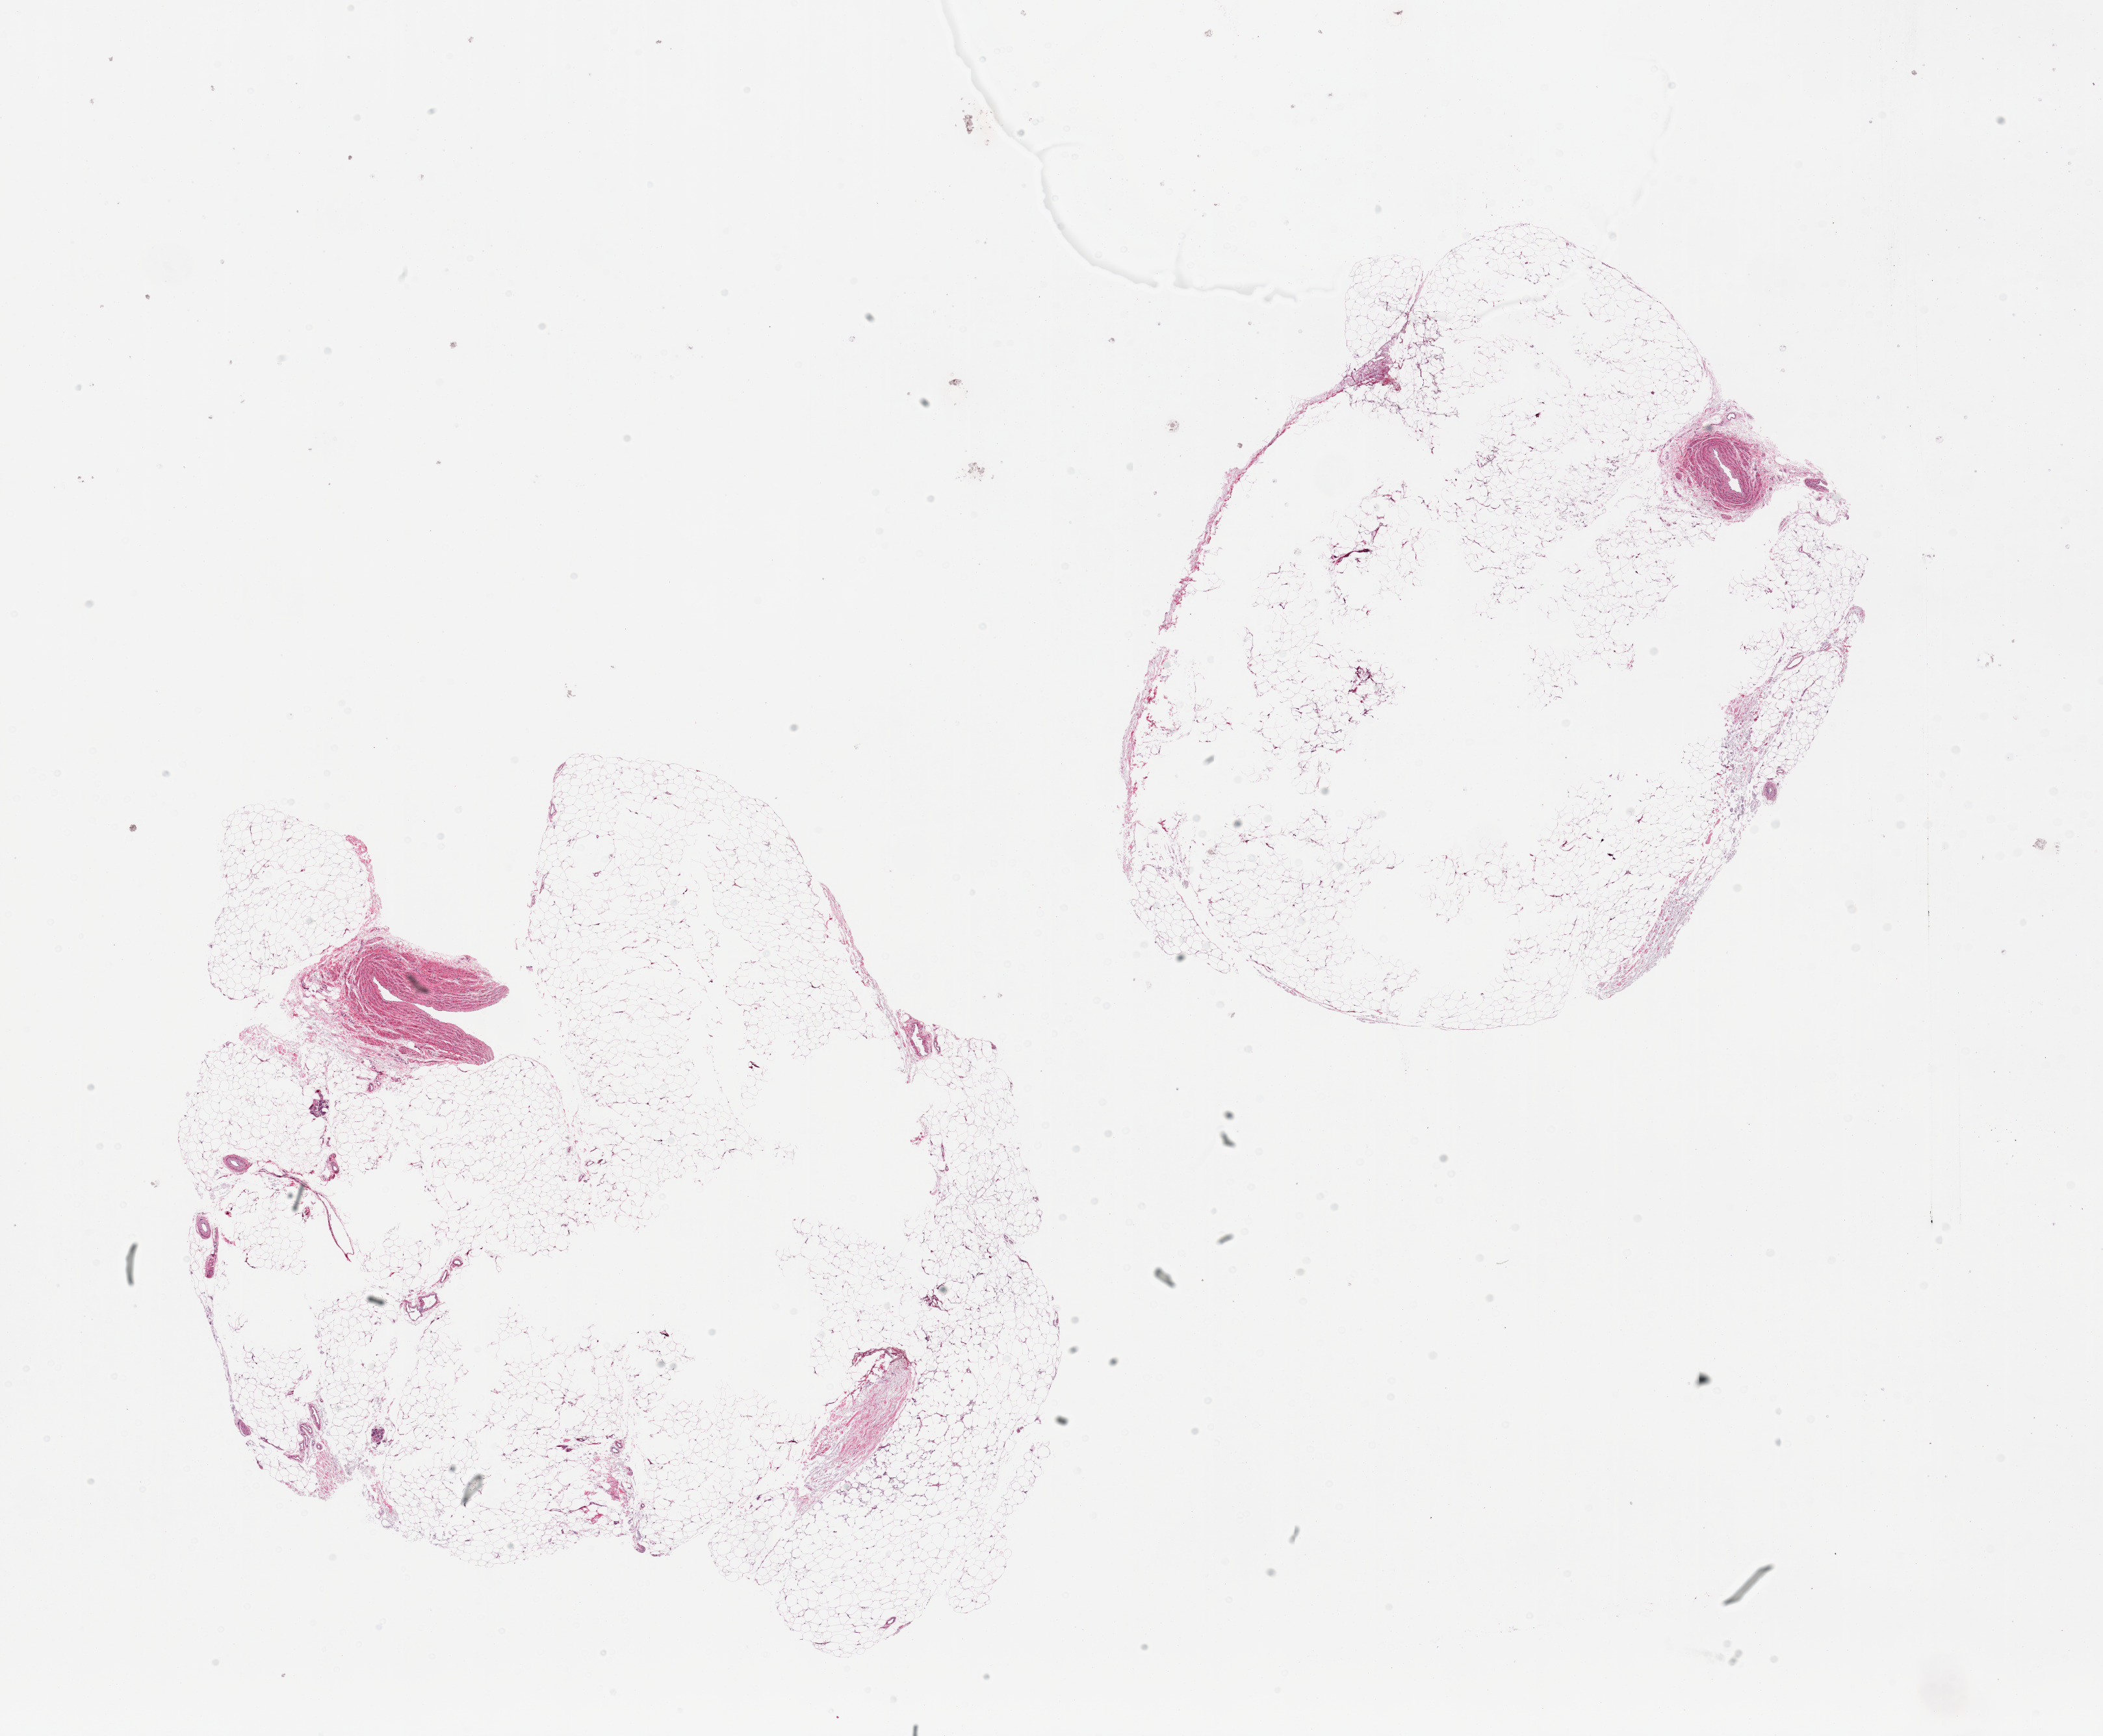
Digitized H&E-stained section, low-resolution overview of the scanned area, about 25.6 x 21.1 mm (acquisition: 20x scan); PAXgene-fixed paraffin-embedded (PFPE) section; target tissue: adipose tissue; tissue donor sample. Female donor.
• pathologist's review note for this sample: 2 pieces; numerous internal holes